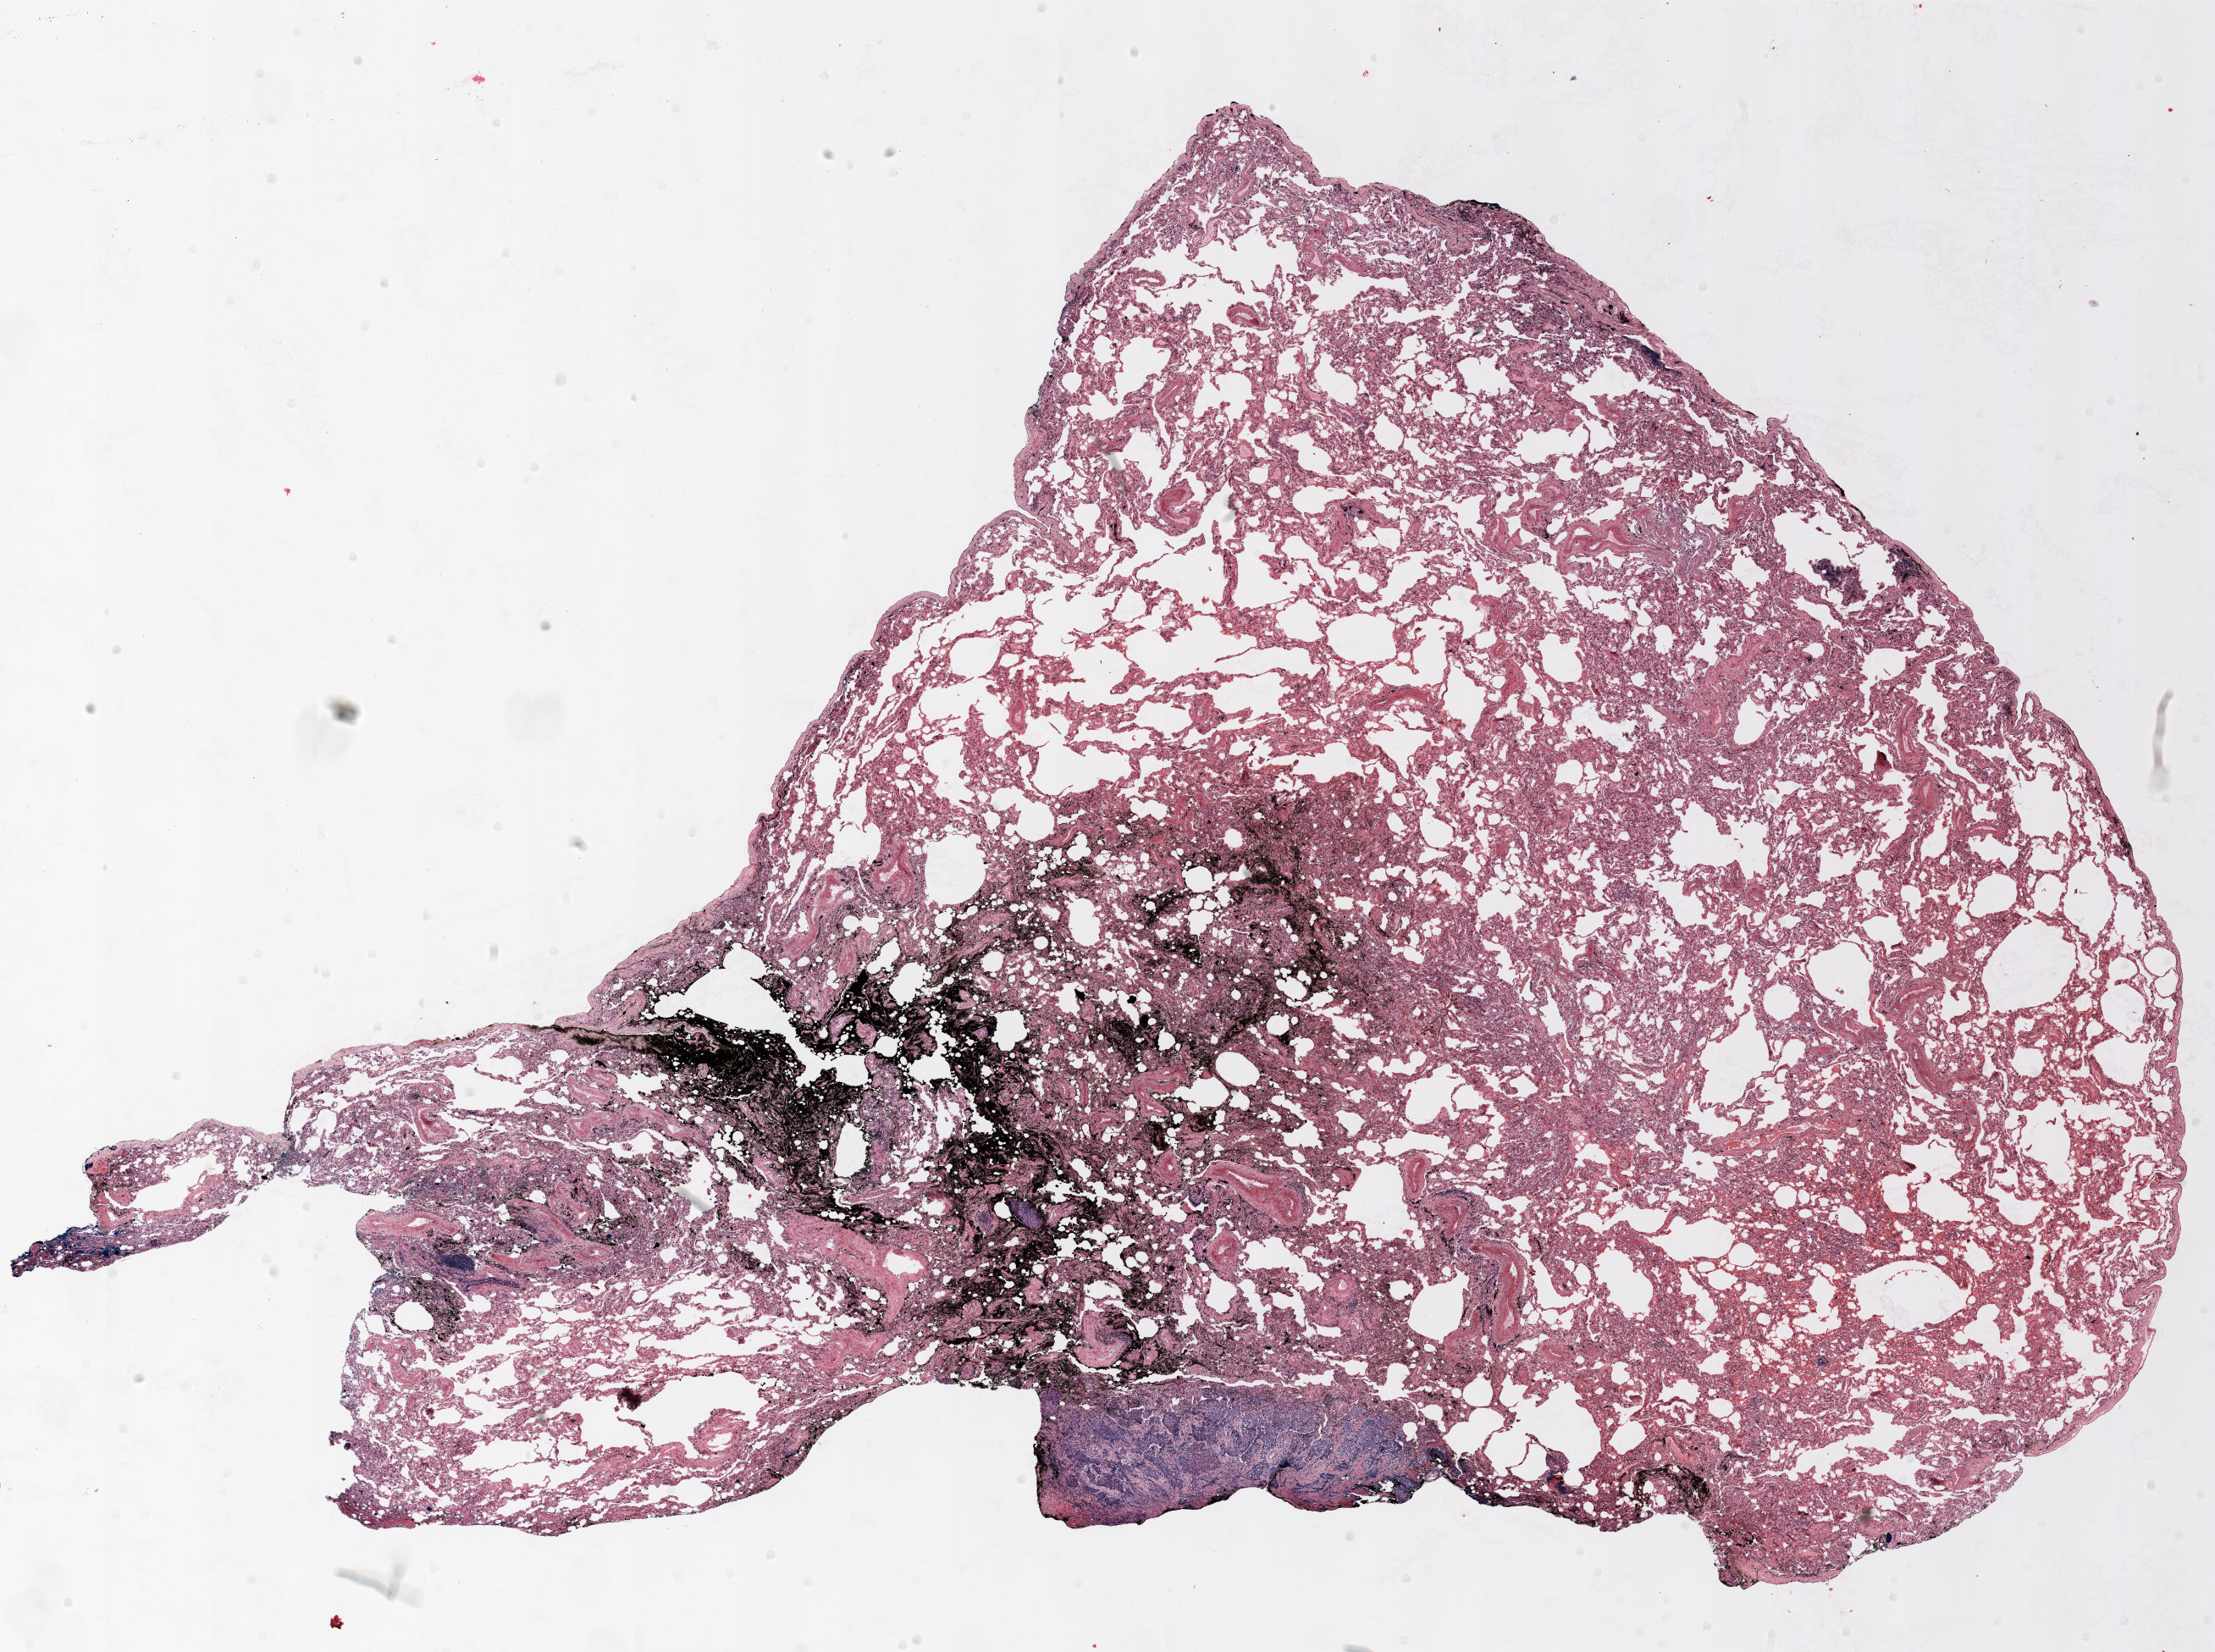
Whole-slide histology image, H&E-stained — whole scanned area (about 21.0 x 15.7 mm, slide scanned at 20x) shown as a low-resolution overview; FFPE section; lung tissue. Male, age 63 at enrolment. Current smoker at enrolment. Grade: poorly differentiated (G3).
- participant's lung-cancer diagnosis: Squamous cell carcinoma, NOS
- tumour size (pathology): 4 mm
- stage (AJCC 6th edition): IA
- primary tumour location (clinical record): left lower lobe